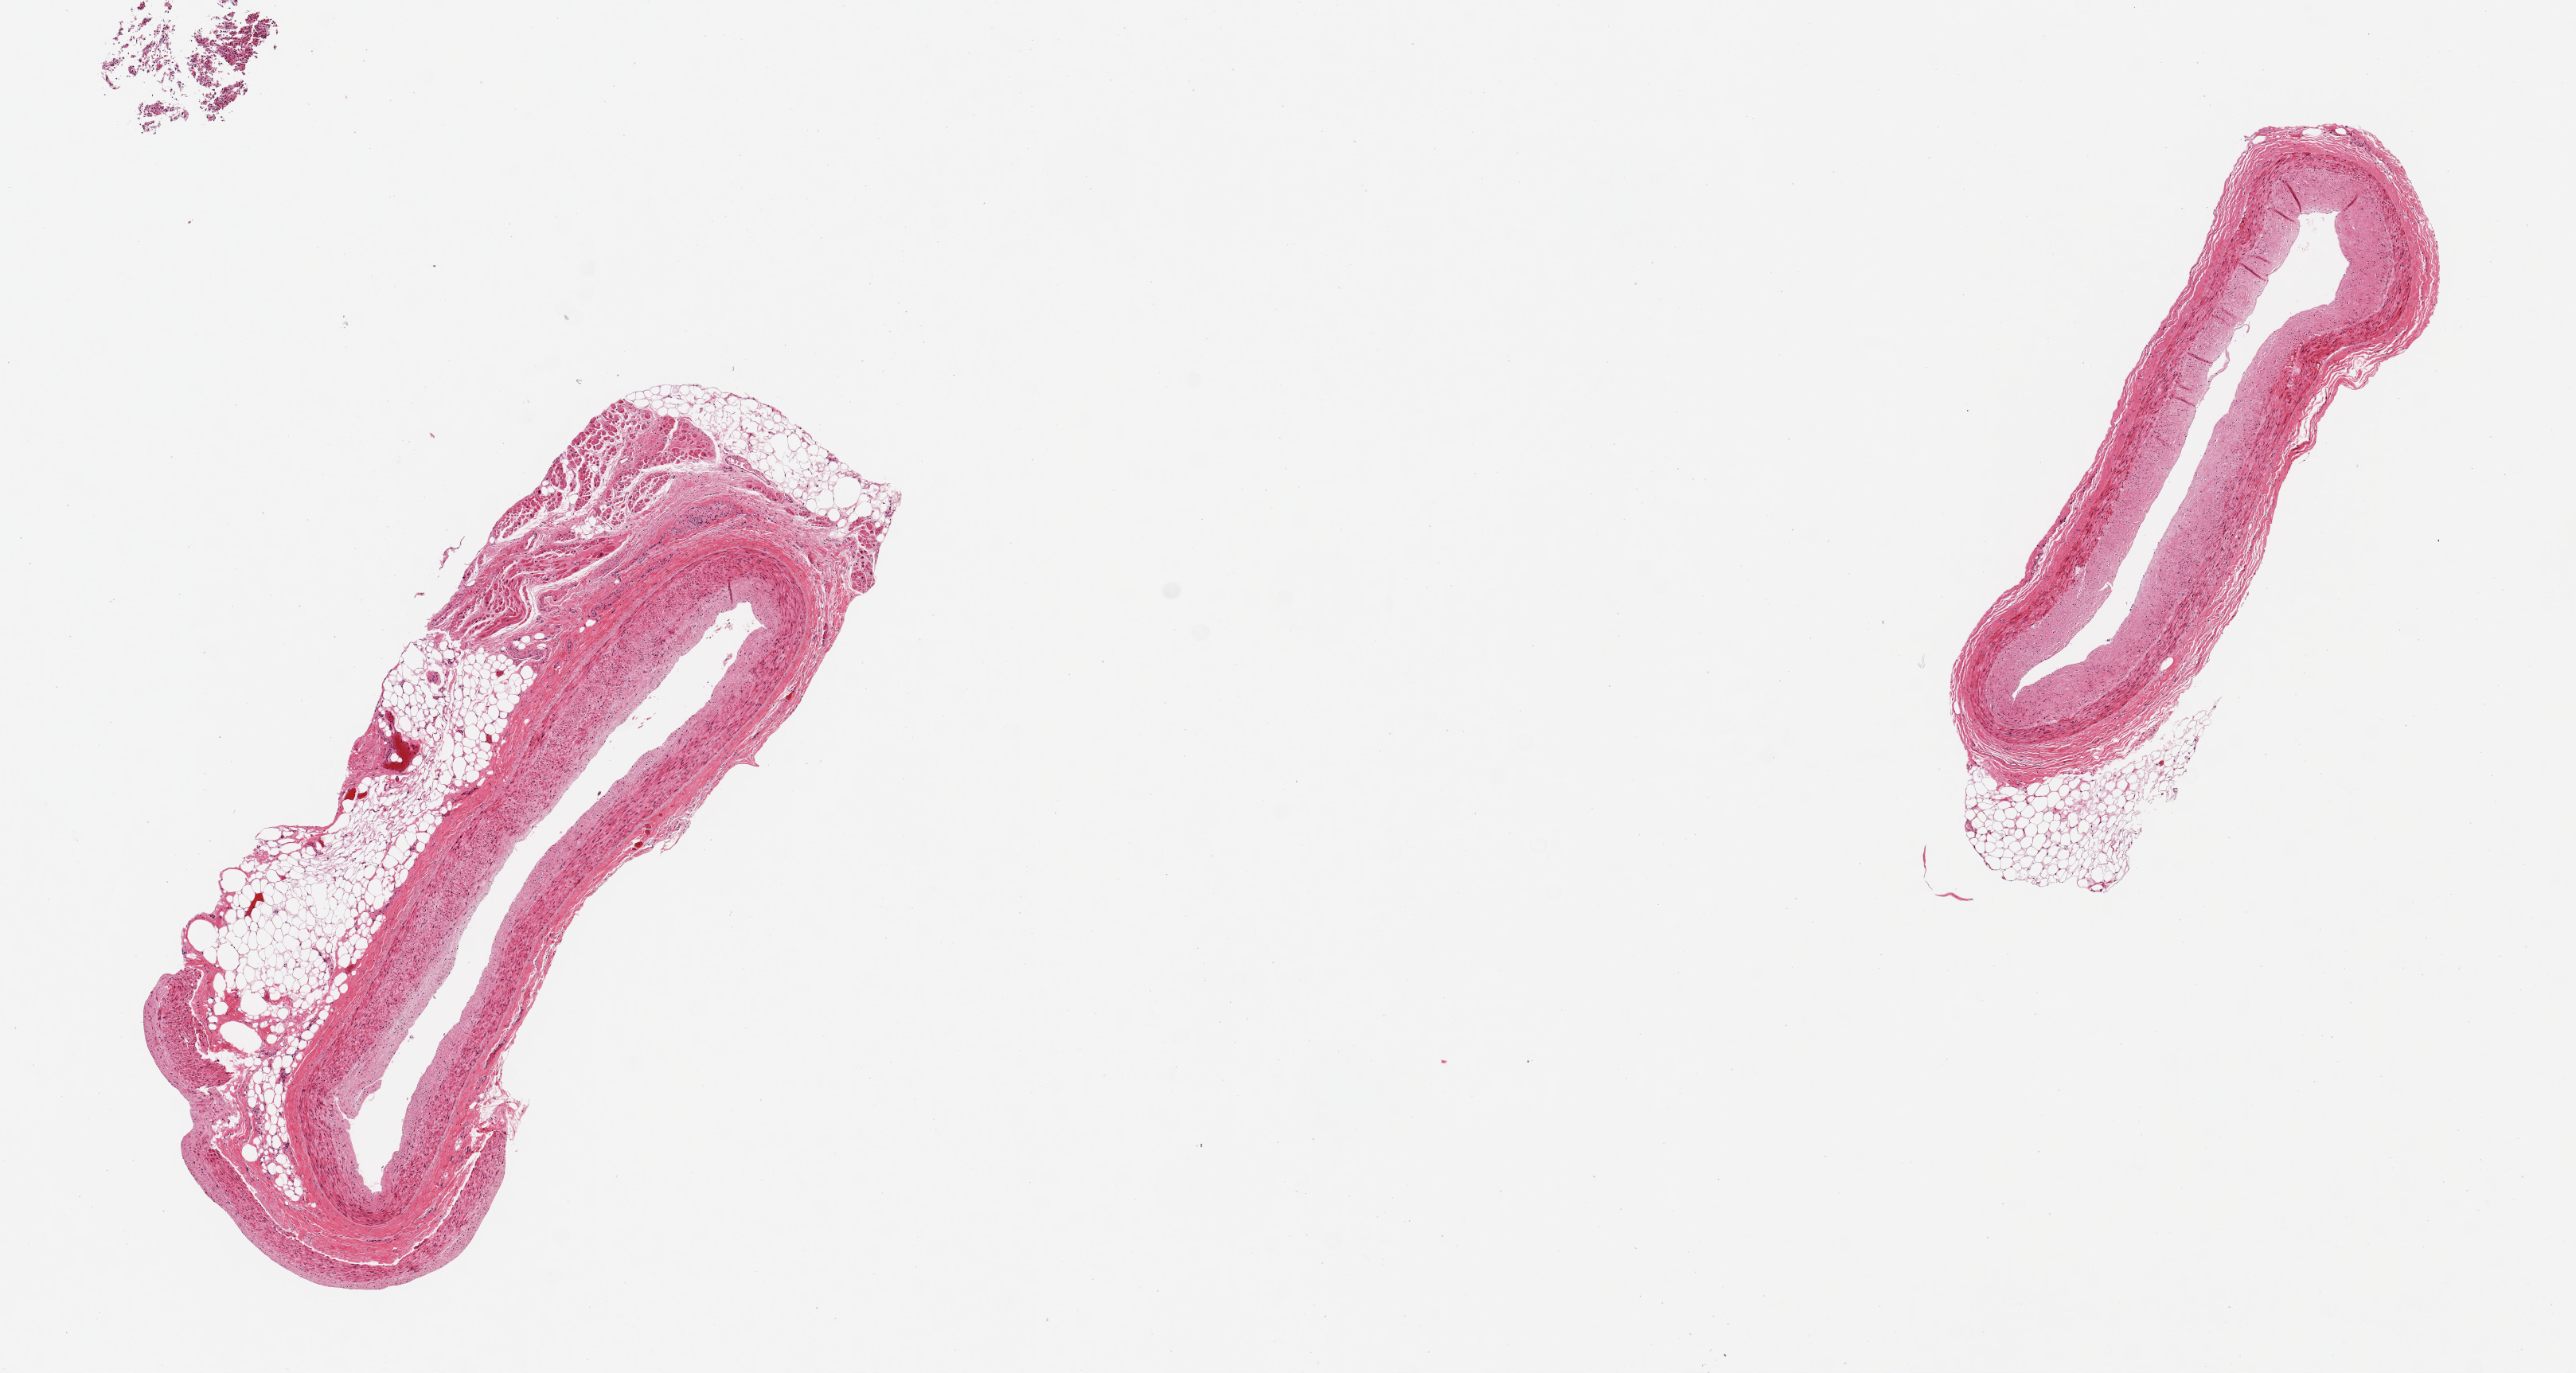
Digitized hematoxylin and eosin (H&E)-stained section, brightfield — a low-resolution overview of the entire scanned area, about 12.8 x 6.8 mm (from a 20x scan). PAXgene-fixed, paraffin-embedded tissue. Sampled site (target tissue): coronary artery. Tissue donor sample. Donor sex: female.
Pathologist's review note for this sample: 2 pieces; external fat 10 & 50%.